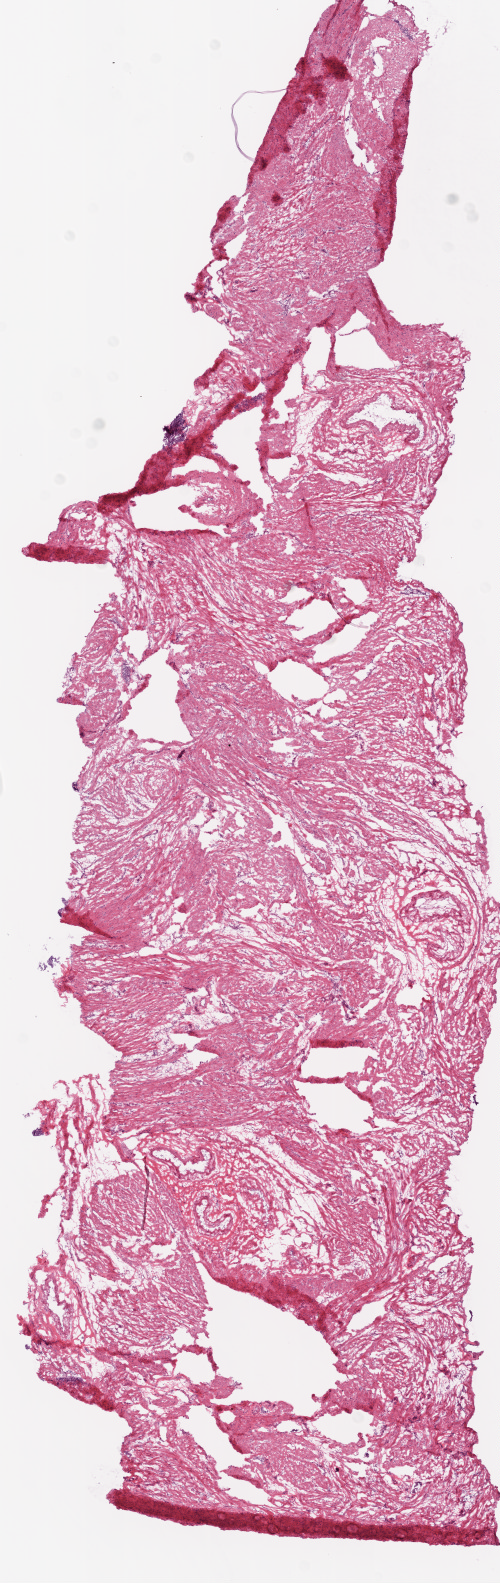
H&E-stained whole-slide image, shown as a low-resolution overview of the whole scanned area (about 4.0 x 12.7 mm, acquisition: 20x scan). Frozen section from the top of the tissue portion. Ovary, solid tissue normal (non-tumour tissue) sample. Female, age 50 years at initial diagnosis.
- this section: solid tissue normal sample (biorepository sample class)
- patient diagnosis: Serous cystadenocarcinoma, NOS